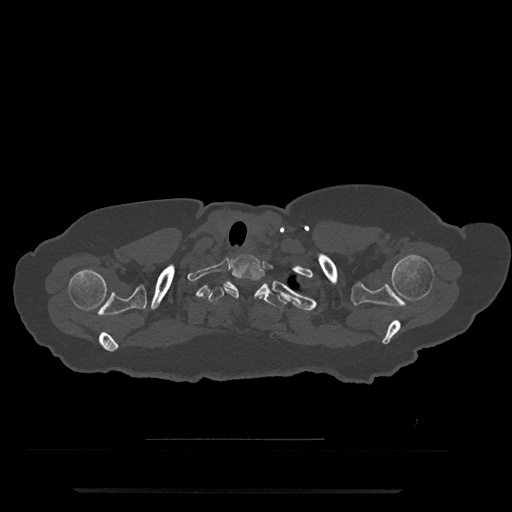
CT including the spine, one axial slice. Reconstruction kernel Br40s/3. 120 kVp. Bone window (W 1800 / L 400 HU). 0.5 mm slice thickness. 512 × 512 image matrix, field of view 440 × 440 mm. Female patient, age 51 years. Case-level facts recorded for this patient, not image findings: primary cancer: neuro; vertebrae with lytic lesions (as recorded): T8.
Structures marked on this image (semi-automatic segmentation, software-assisted and operator-edited):
- T1 vertebra: bounding box (x1, y1, x2, y2) in pixels: (223, 254, 265, 298)
- T2 vertebra: (207, 281, 286, 309)